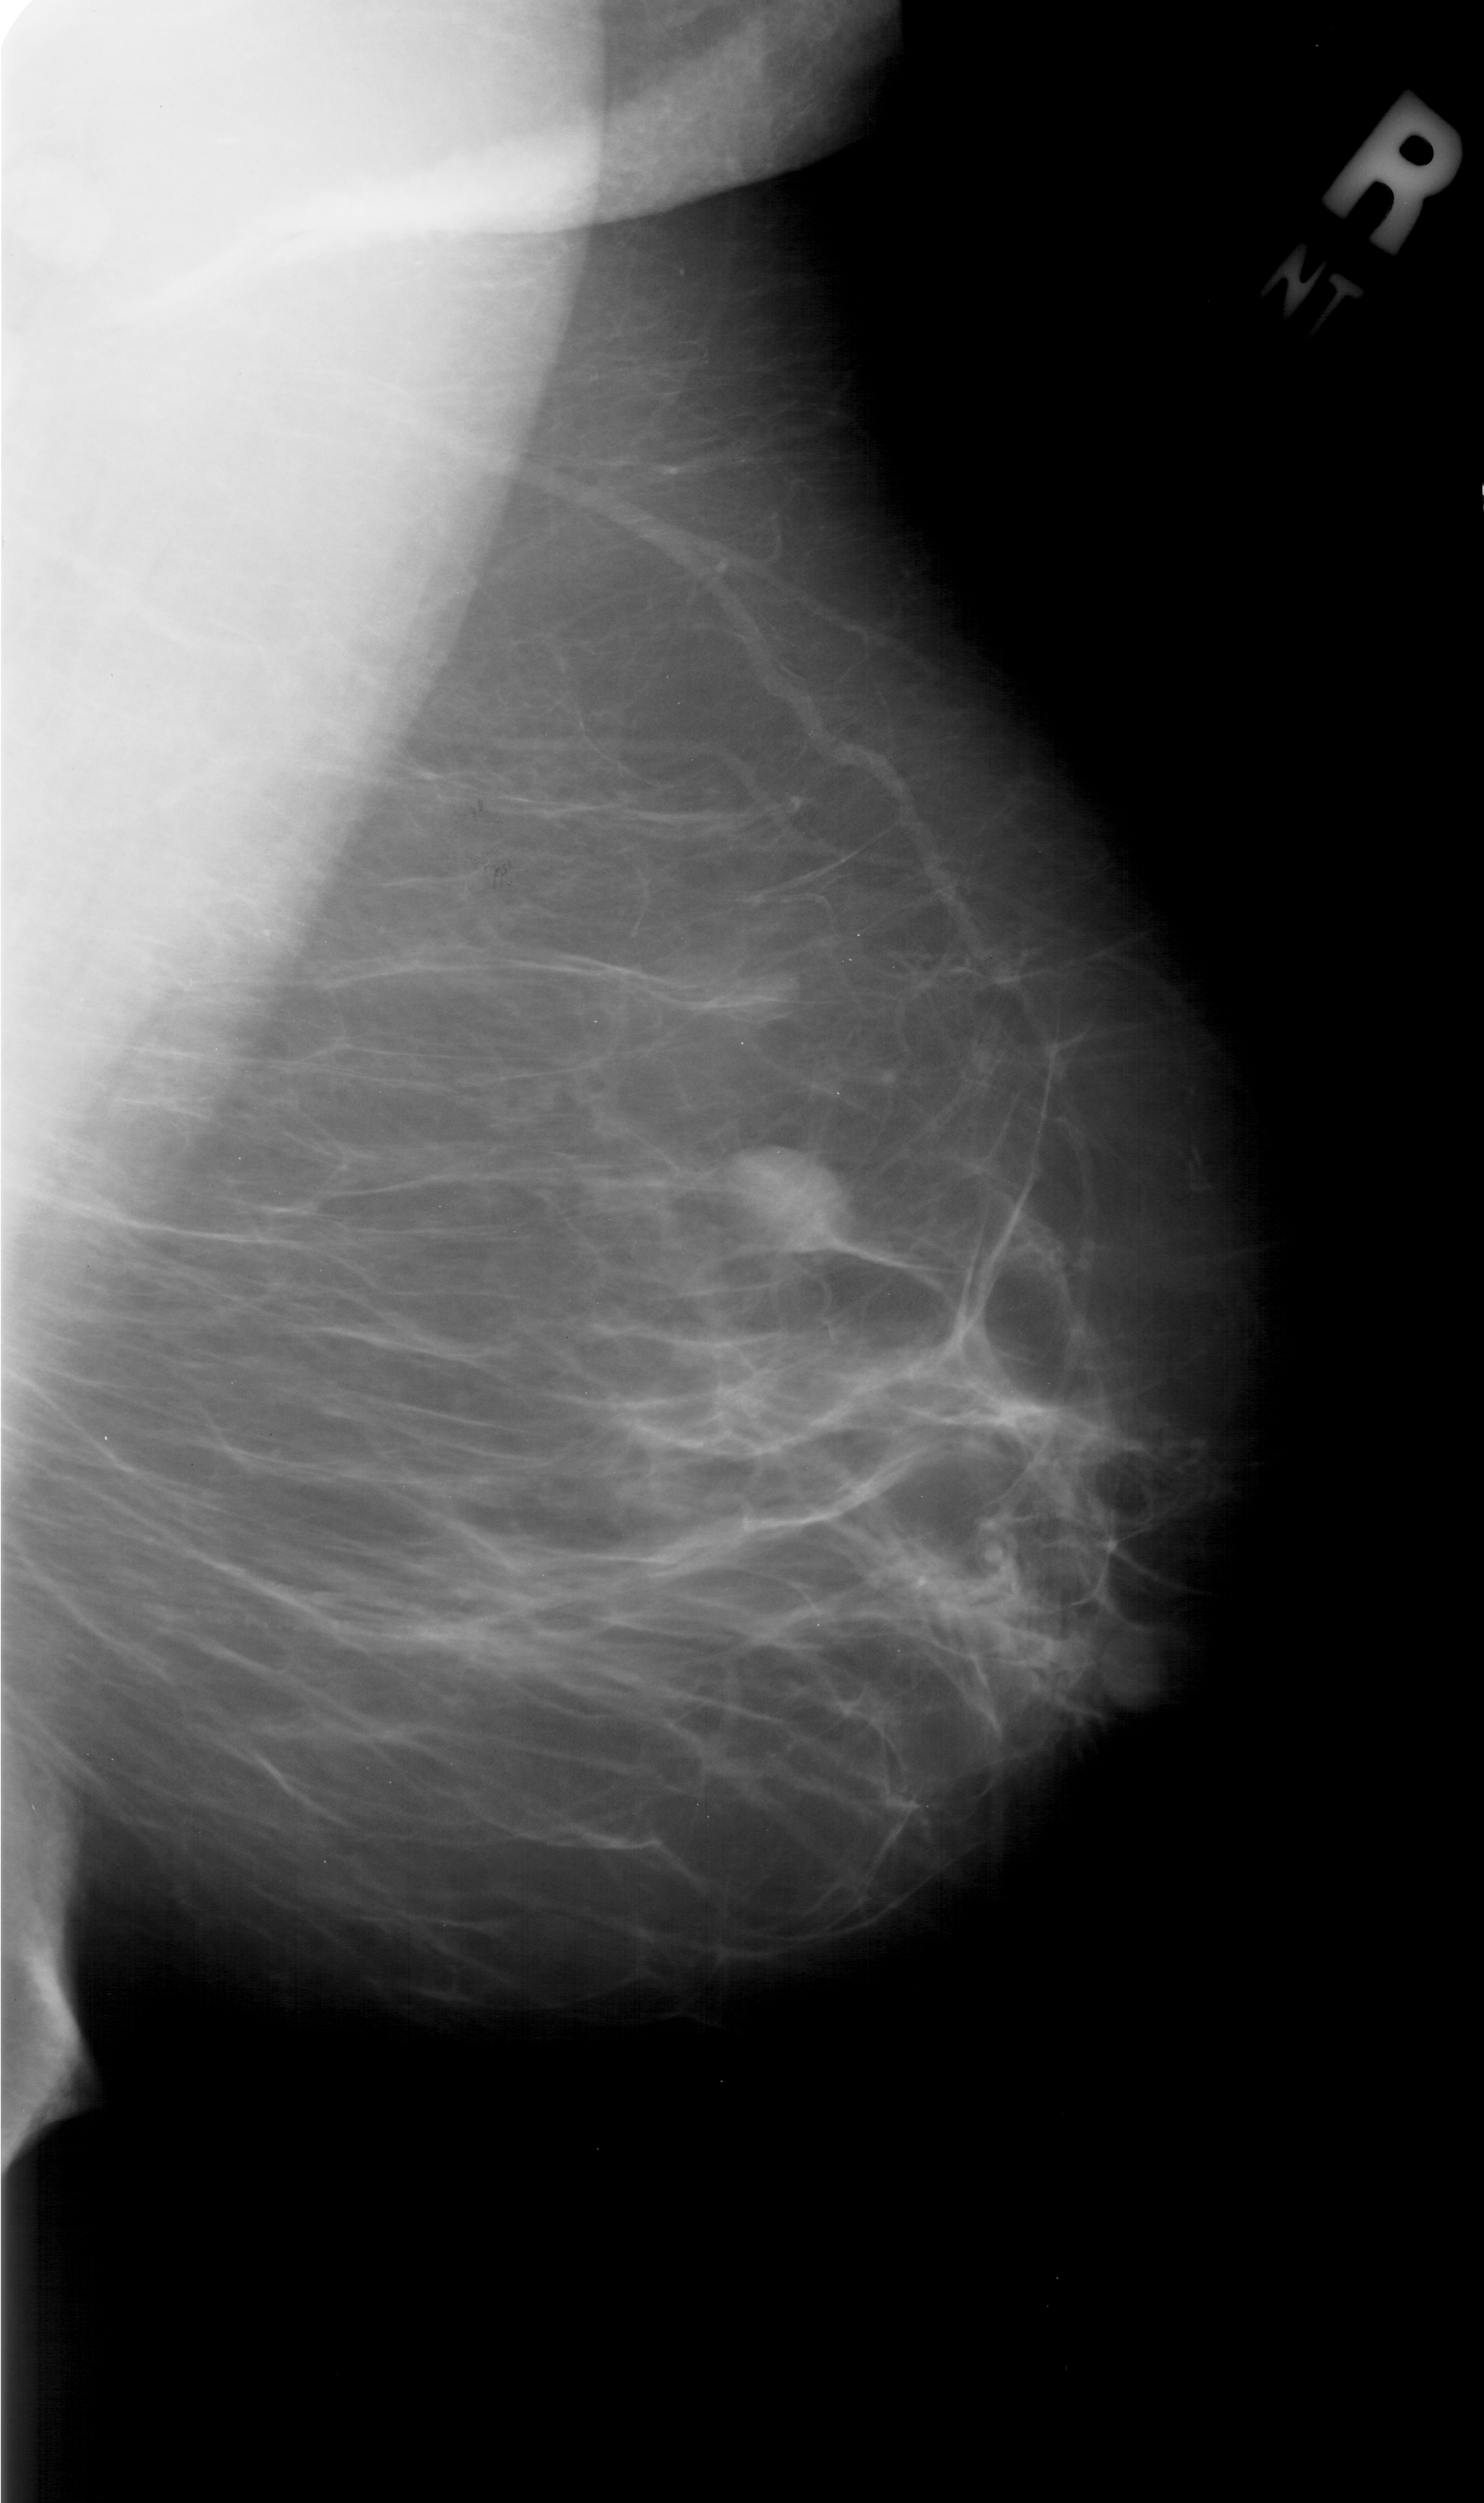
Mammogram (digitized film); right breast; mediolateral oblique (MLO) view; breast composition: almost entirely fatty (BI-RADS density category 1 of 4); 1484 × 2503 image matrix.
Marked abnormalities (boxes around the expert regions of interest):
- mass, shape oval, margins obscured; BI-RADS assessment category 4; pathology result (as recorded, not read from the image): benign: bounding box <732,1147,843,1228> (left, top, right, bottom; pixels)